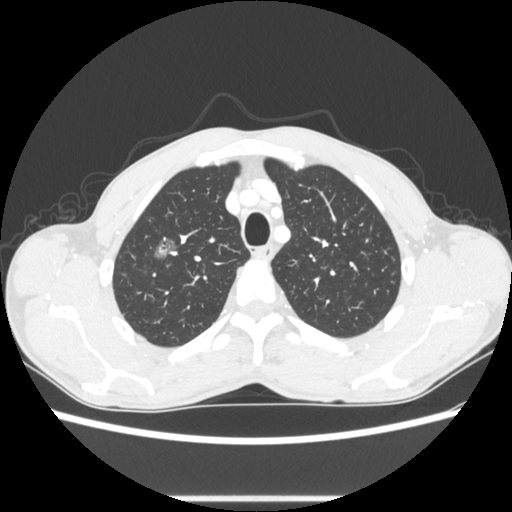
Chest CT, one axial slice. Position 230 of 289 along the scan axis. Reconstruction kernel STANDARD. 100 kVp. Lung window (W 1500 / L -600 HU). 512 × 512 image matrix, field of view 350 × 350 mm. Male patient, age 54 years. Case-level facts recorded for this patient, not image findings: clinical TNM (as recorded): T1a N0 M0.
Structures marked on this image (rectangle marked by the reading radiologist):
- lung tumour (recorded histology: adenocarcinoma): bounding box (x1, y1, x2, y2) in pixels: (150, 233, 176, 262)